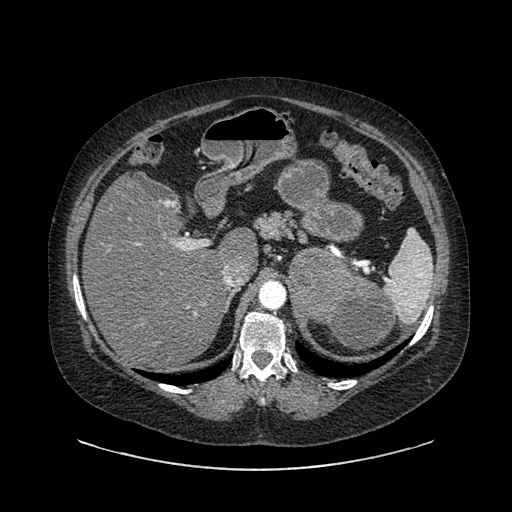
Contrast-enhanced abdominal CT, one axial slice. Slice 603 of 769 in the series (ordered by position). Intravenous contrast given. Soft-tissue window (W 400 / L 40 HU). 512 × 512 image matrix, field of view 460 × 460 mm. Patient: female, 61 years. Case-level facts recorded for this patient, not image findings: diagnosis: adrenocortical carcinoma; tumour side: left adrenal; tumour size at pathology: 13 cm; Ki-67 index: 79 %; stage (as recorded): 2.
Annotated regions visible in this slice (semi-automatic segmentation, software-assisted and operator-edited):
- mass: bounding box (x1, y1, x2, y2) in pixels: (290, 251, 395, 349)